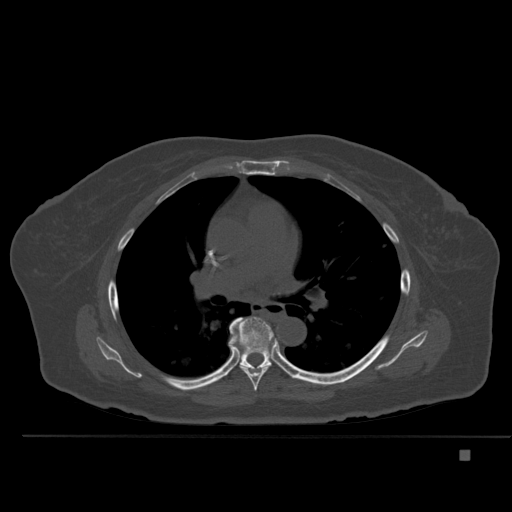
CT including the spine, one axial slice; position 333 of 477 along the scan axis; bone window (W 1800 / L 400 HU); 1.5 mm slice thickness; 512 × 512 image matrix, field of view 422 × 422 mm. Patient: female, 74 years. From the clinical record (not read from this slice): primary cancer: colon.
Outlined on this slice (semi-automatic segmentation, software-assisted and operator-edited):
- T6 vertebra: bounding box <240,365,269,391> (left, top, right, bottom; pixels)
- T7 vertebra: <229,317,286,372>